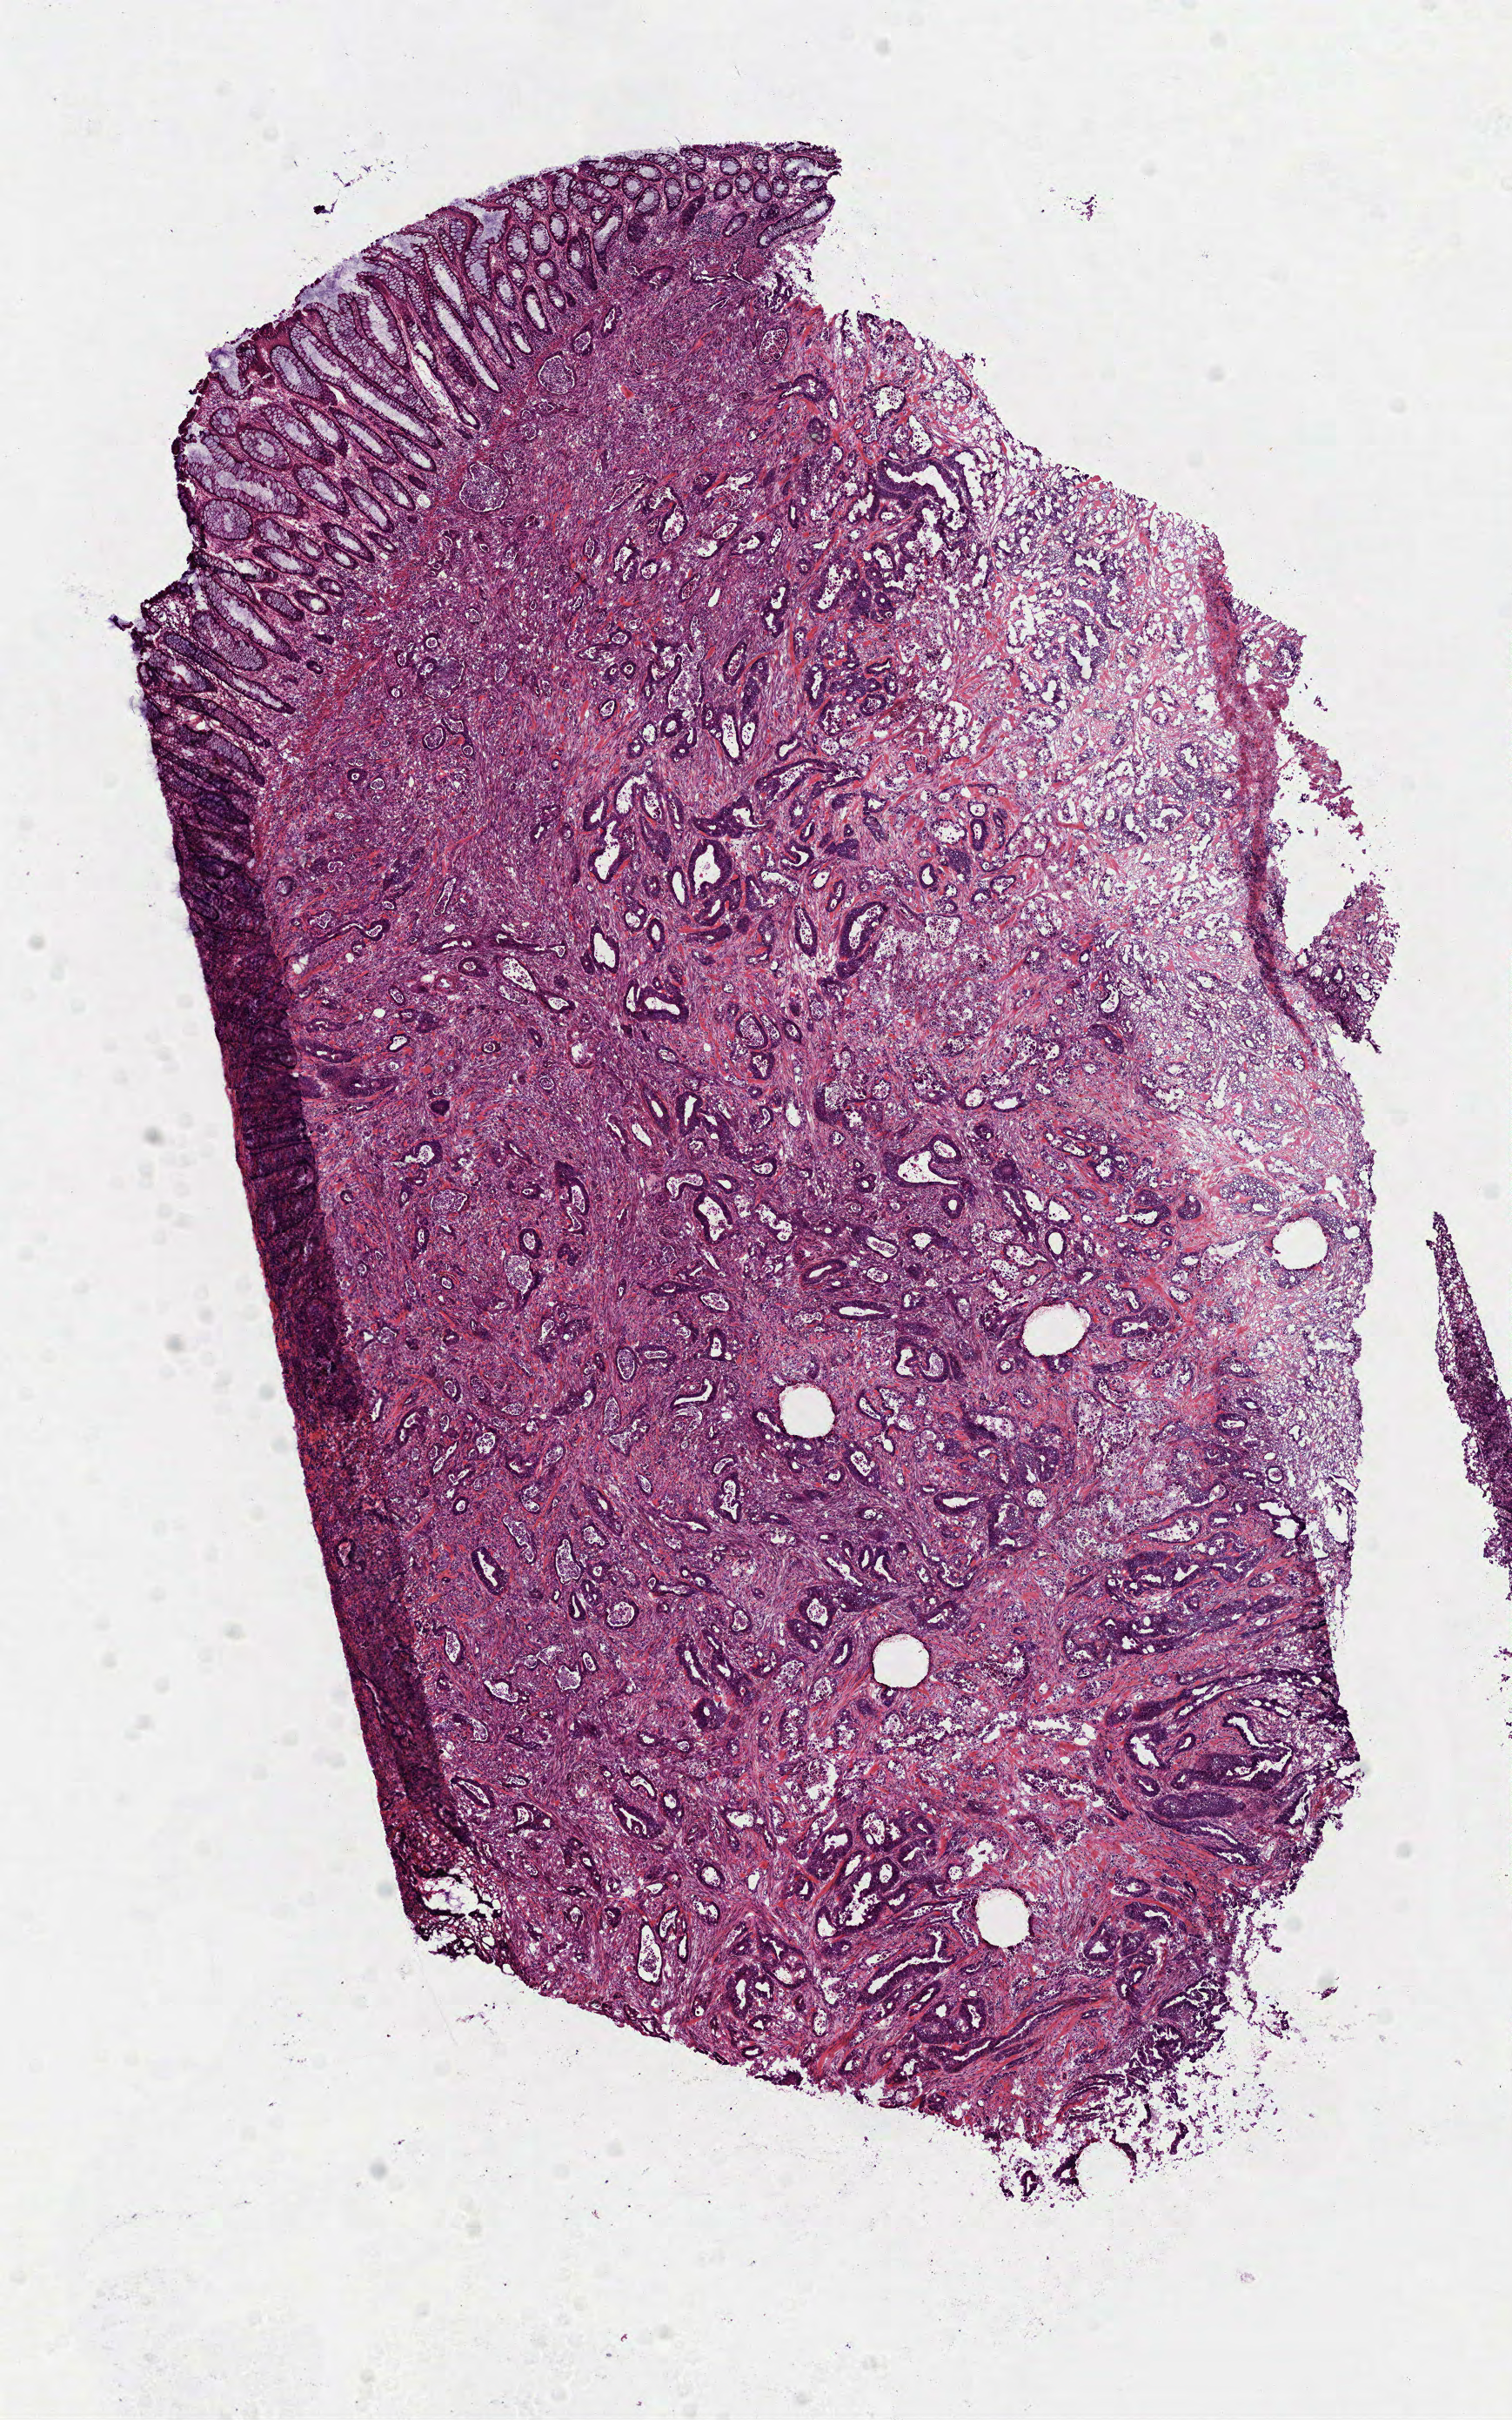
Whole-slide histology image, Hematoxylin and eosin (H&E) stained — a low-resolution overview of the entire scanned area, about 7.0 x 11.2 mm (from a 40x scan). Frozen section from the top of the tissue portion. Primary tumour sample from the rectum. Patient: male, age at initial diagnosis 60 years. Slide review estimates, as recorded: tumour cells 60%, tumour nuclei 60%, normal cells 8%, stromal cells 22%, necrosis 10%. Infiltration values recorded for this section: lymphocyte infiltration 10%.
Pathologic diagnosis: Adenocarcinoma, NOS (rectosigmoid junction). Lymph nodes positive (case pathology): 3 of 20 examined.